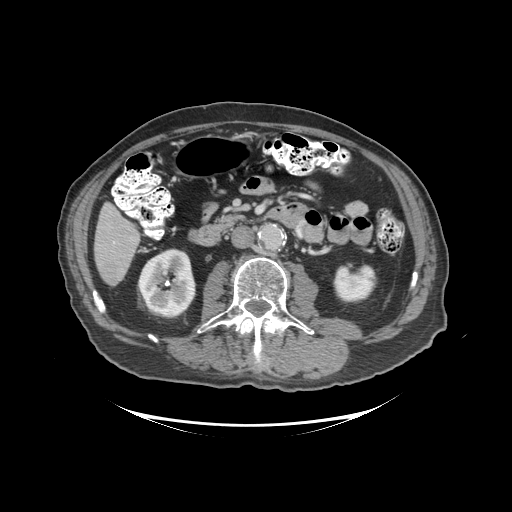
Contrast-enhanced abdominal CT (liver protocol), one axial slice. Position 32 of 99 along the scan axis. 140 kVp. Soft-tissue window (W 400 / L 40 HU). 2.5 mm slice thickness. 512 × 512 image matrix, field of view 460 × 460 mm. From the clinical record (not read from this slice): diagnosis: hepatocellular carcinoma (patient treated with transarterial chemoembolisation; whether this scan precedes or follows treatment is not stated here); TNM stage (as recorded): Stage-I; Child-Pugh class: A; tumour differentiation: moderately differentiated; tumour nodularity: uninodular.
Structures marked on this image (semi-automatically segmented with operator editing):
- liver parenchyma outside the tumour (the mass and vessels are separate outlines, so this box may not span the whole liver): bounding box [x1, y1, x2, y2] px = [94, 202, 140, 286]